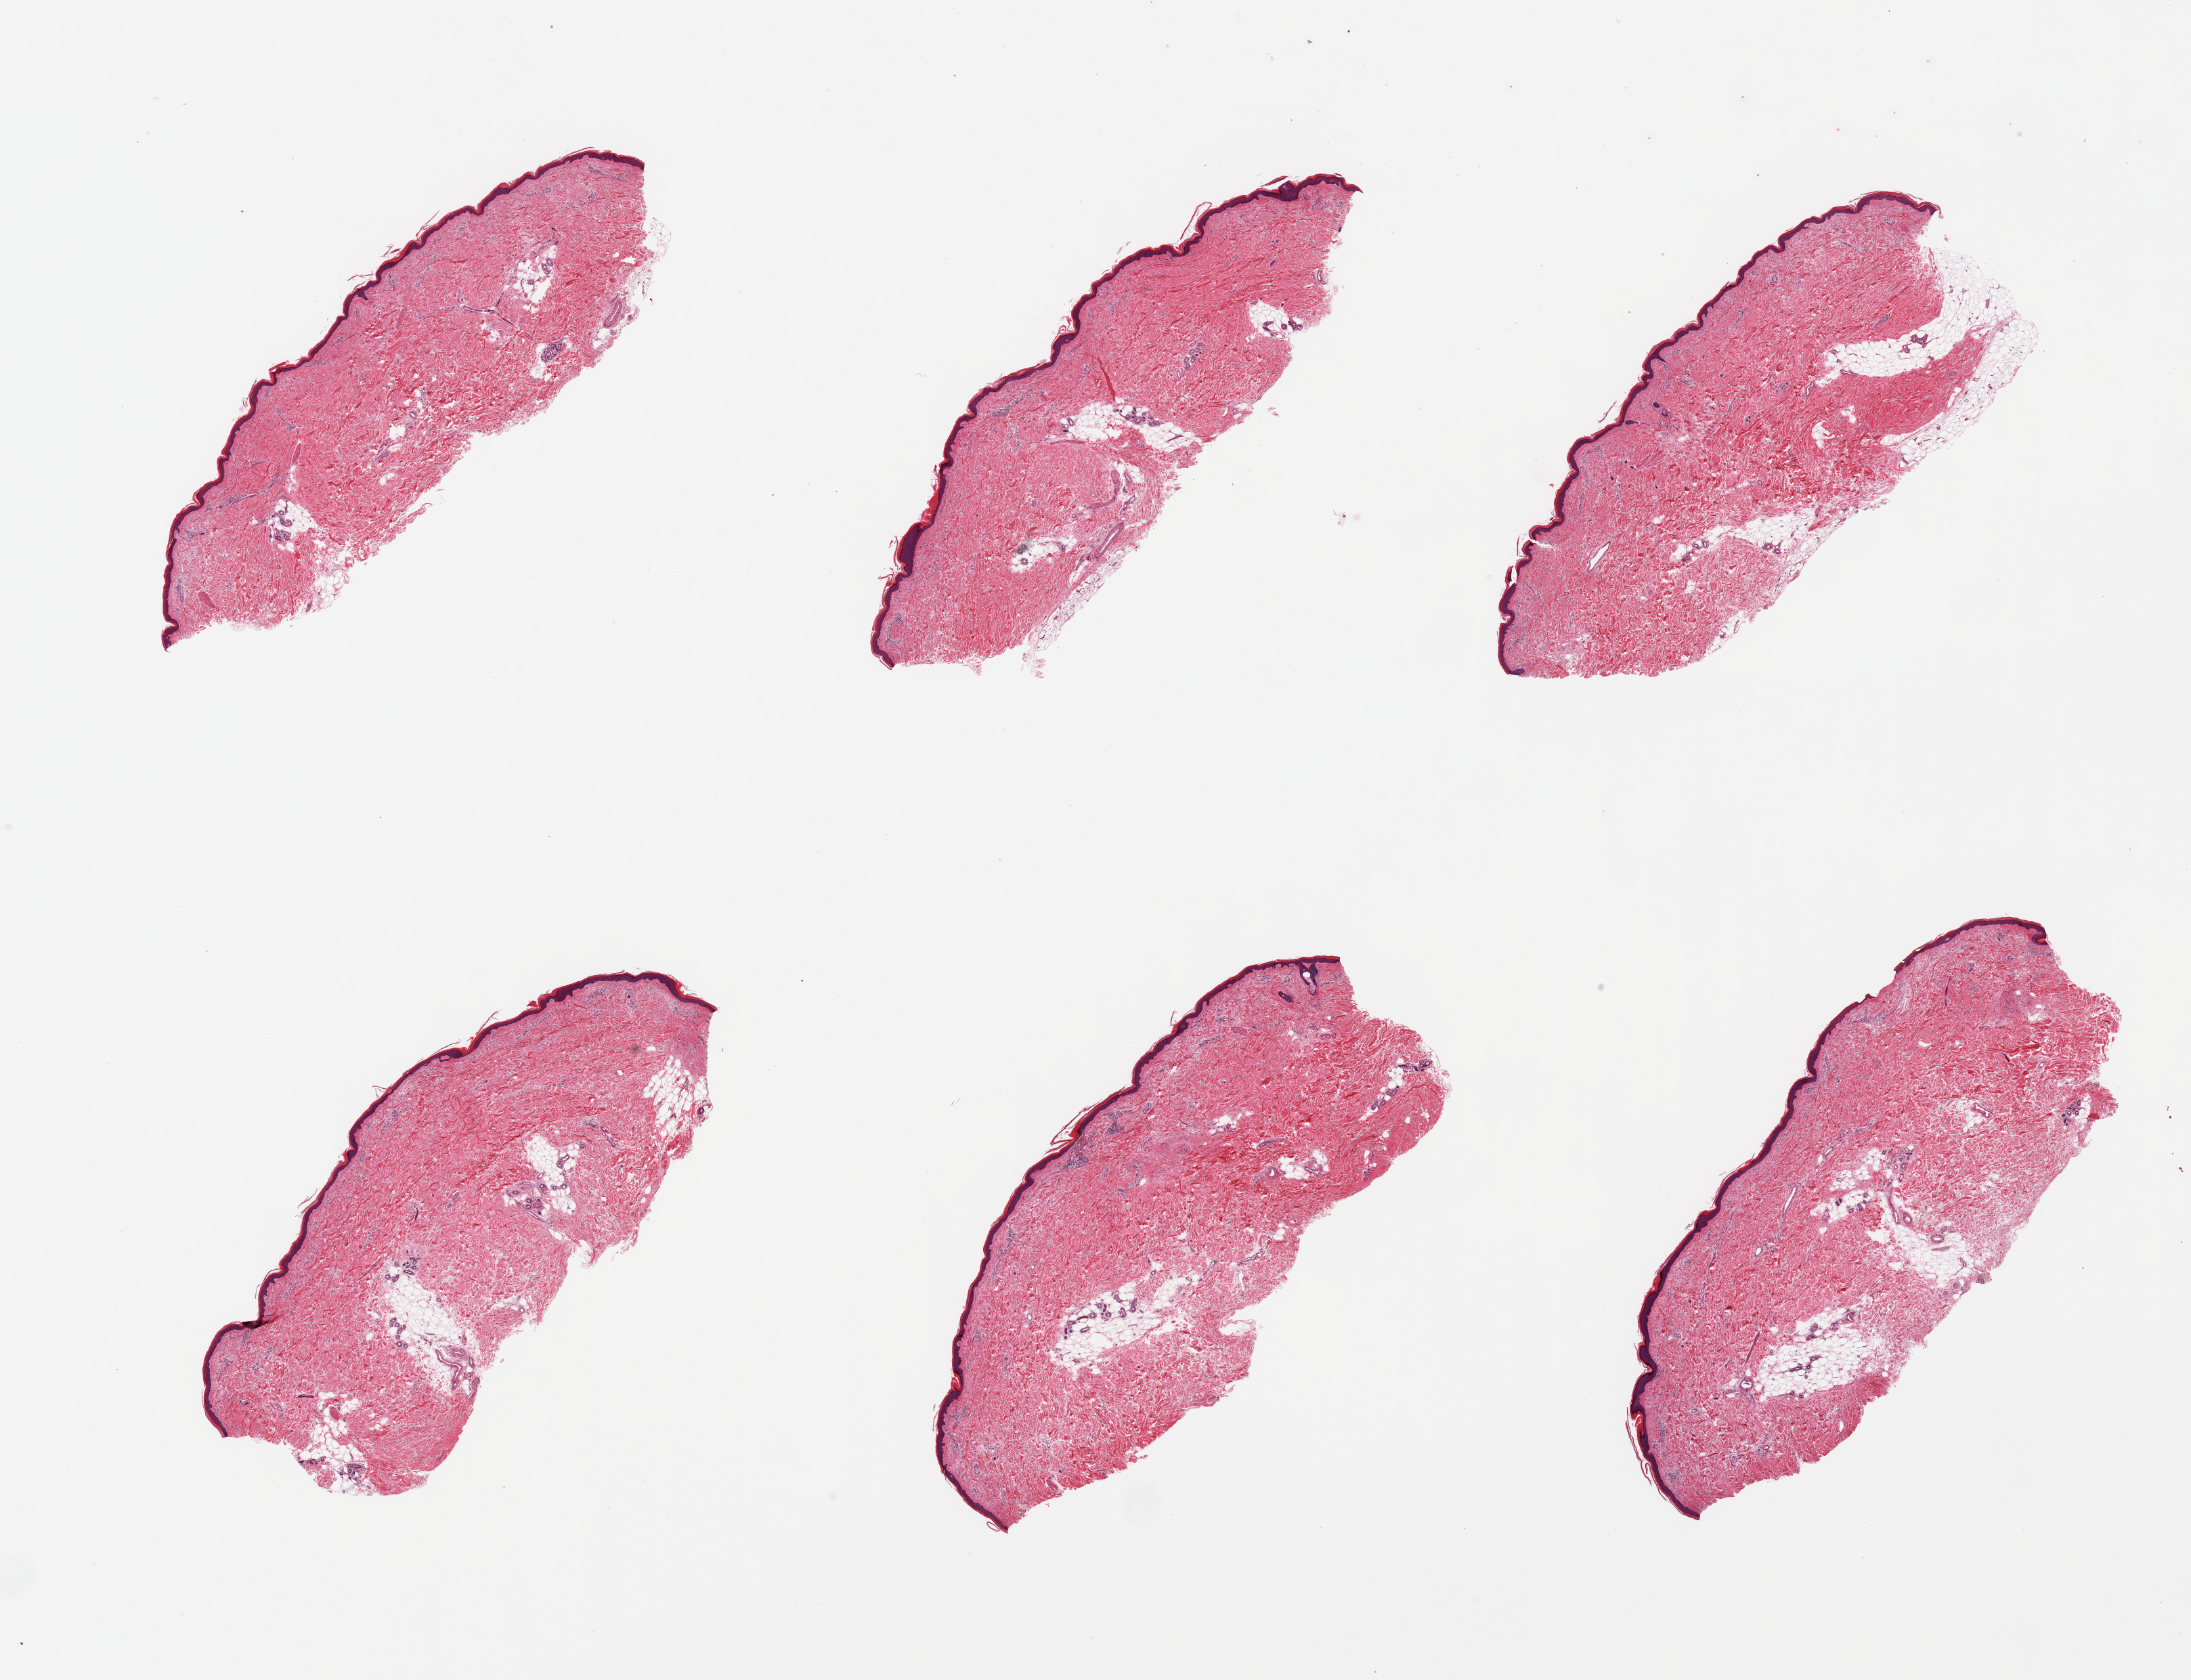
Digitized haematoxylin and eosin-stained section, brightfield — a low-resolution overview of the entire scanned area, about 25.6 x 19.6 mm (from a 20x scan), PAXgene-fixed paraffin-embedded (PFPE) section, target tissue: skin of lower leg, tissue donor sample. Donor sex: male.
Pathologist's review note for this sample: 6 pieces, minimal dermal fat; squamous epithelium is ~60 microns.